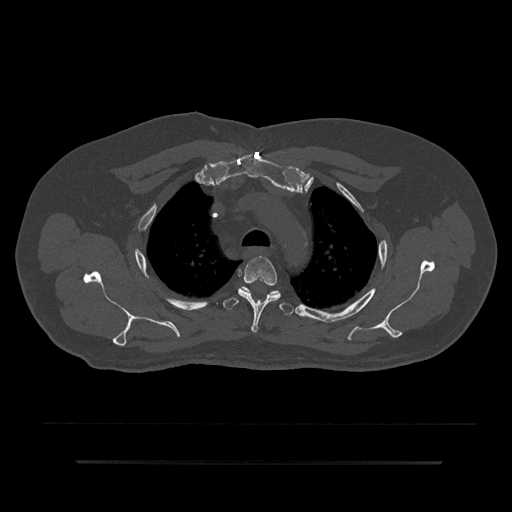
CT including the spine, one axial slice; reconstruction kernel Br40s/3; 120 kVp; bone window (W 1800 / L 400 HU); 0.5 mm slice thickness; 512 × 512 image matrix. Patient: male, 59 years. From the clinical record (not read from this slice): primary cancer: bile ducts; vertebrae with lytic lesions (as recorded): T10.
Outlined on this slice (semi-automatic segmentation, software-assisted and operator-edited):
- T3 vertebra: bounding box <238,256,281,333> (left, top, right, bottom; pixels)
- T4 vertebra: <223,287,295,315>